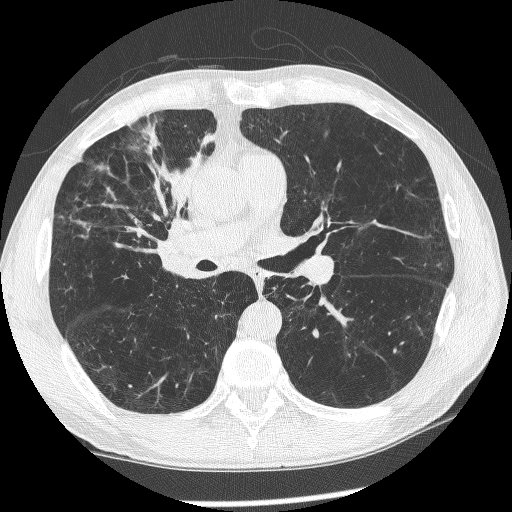
Low-dose screening chest CT, axial slice. First (baseline) screen. Lung window (W 1500 / L -600 HU). 1.25 mm slice thickness. Lung (sharp) reconstruction kernel (BONE). 120 kVp. Slice 137 of 266 in the series. 512 × 512 image matrix, field of view 340 × 340 mm. Male, age 60 years at enrolment. Current smoker at enrolment.
• Lesion marked by an expert reader, bounding box <146,179,216,273> (left, top, right, bottom; pixels).
• Reader record for this screening exam (exam-level; its link to the box is not recorded): non-calcified nodule or mass ≥4 mm, right upper lobe, 12 × 8 mm, spiculated (stellate) margins, mixed attenuation.
• Lung cancer was diagnosed 208 days after this screen: squamous cell carcinoma, NOS, right upper lobe, right middle lobe, right main stem bronchus, poorly differentiated (G3), stage IV (AJCC 6th edition).